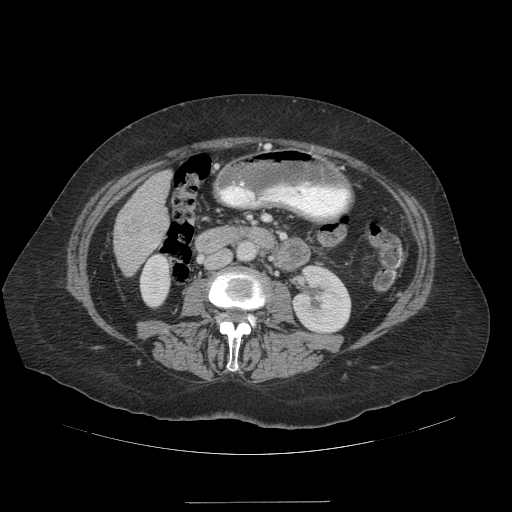
Contrast-enhanced abdominal CT (liver protocol), one axial slice; slice 37 of 99 in the series (ordered by position); soft-tissue window (W 400 / L 40 HU); 2.5 mm slice thickness; 512 × 512 image matrix, field of view 440 × 440 mm. From the clinical record (not read from this slice): diagnosis: hepatocellular carcinoma (patient treated with transarterial chemoembolisation; whether this scan precedes or follows treatment is not stated here); TNM stage (as recorded): Stage-IVA; Child-Pugh class: A; tumour nodularity: multinodular.
Annotated regions visible in this slice (semi-automatic segmentation, software-assisted and operator-edited):
- liver parenchyma outside the tumour (the mass and vessels are separate outlines, so this box may not span the whole liver): bounding box <114,170,170,274> (left, top, right, bottom; pixels)
- liver vessels: <154,244,156,246>